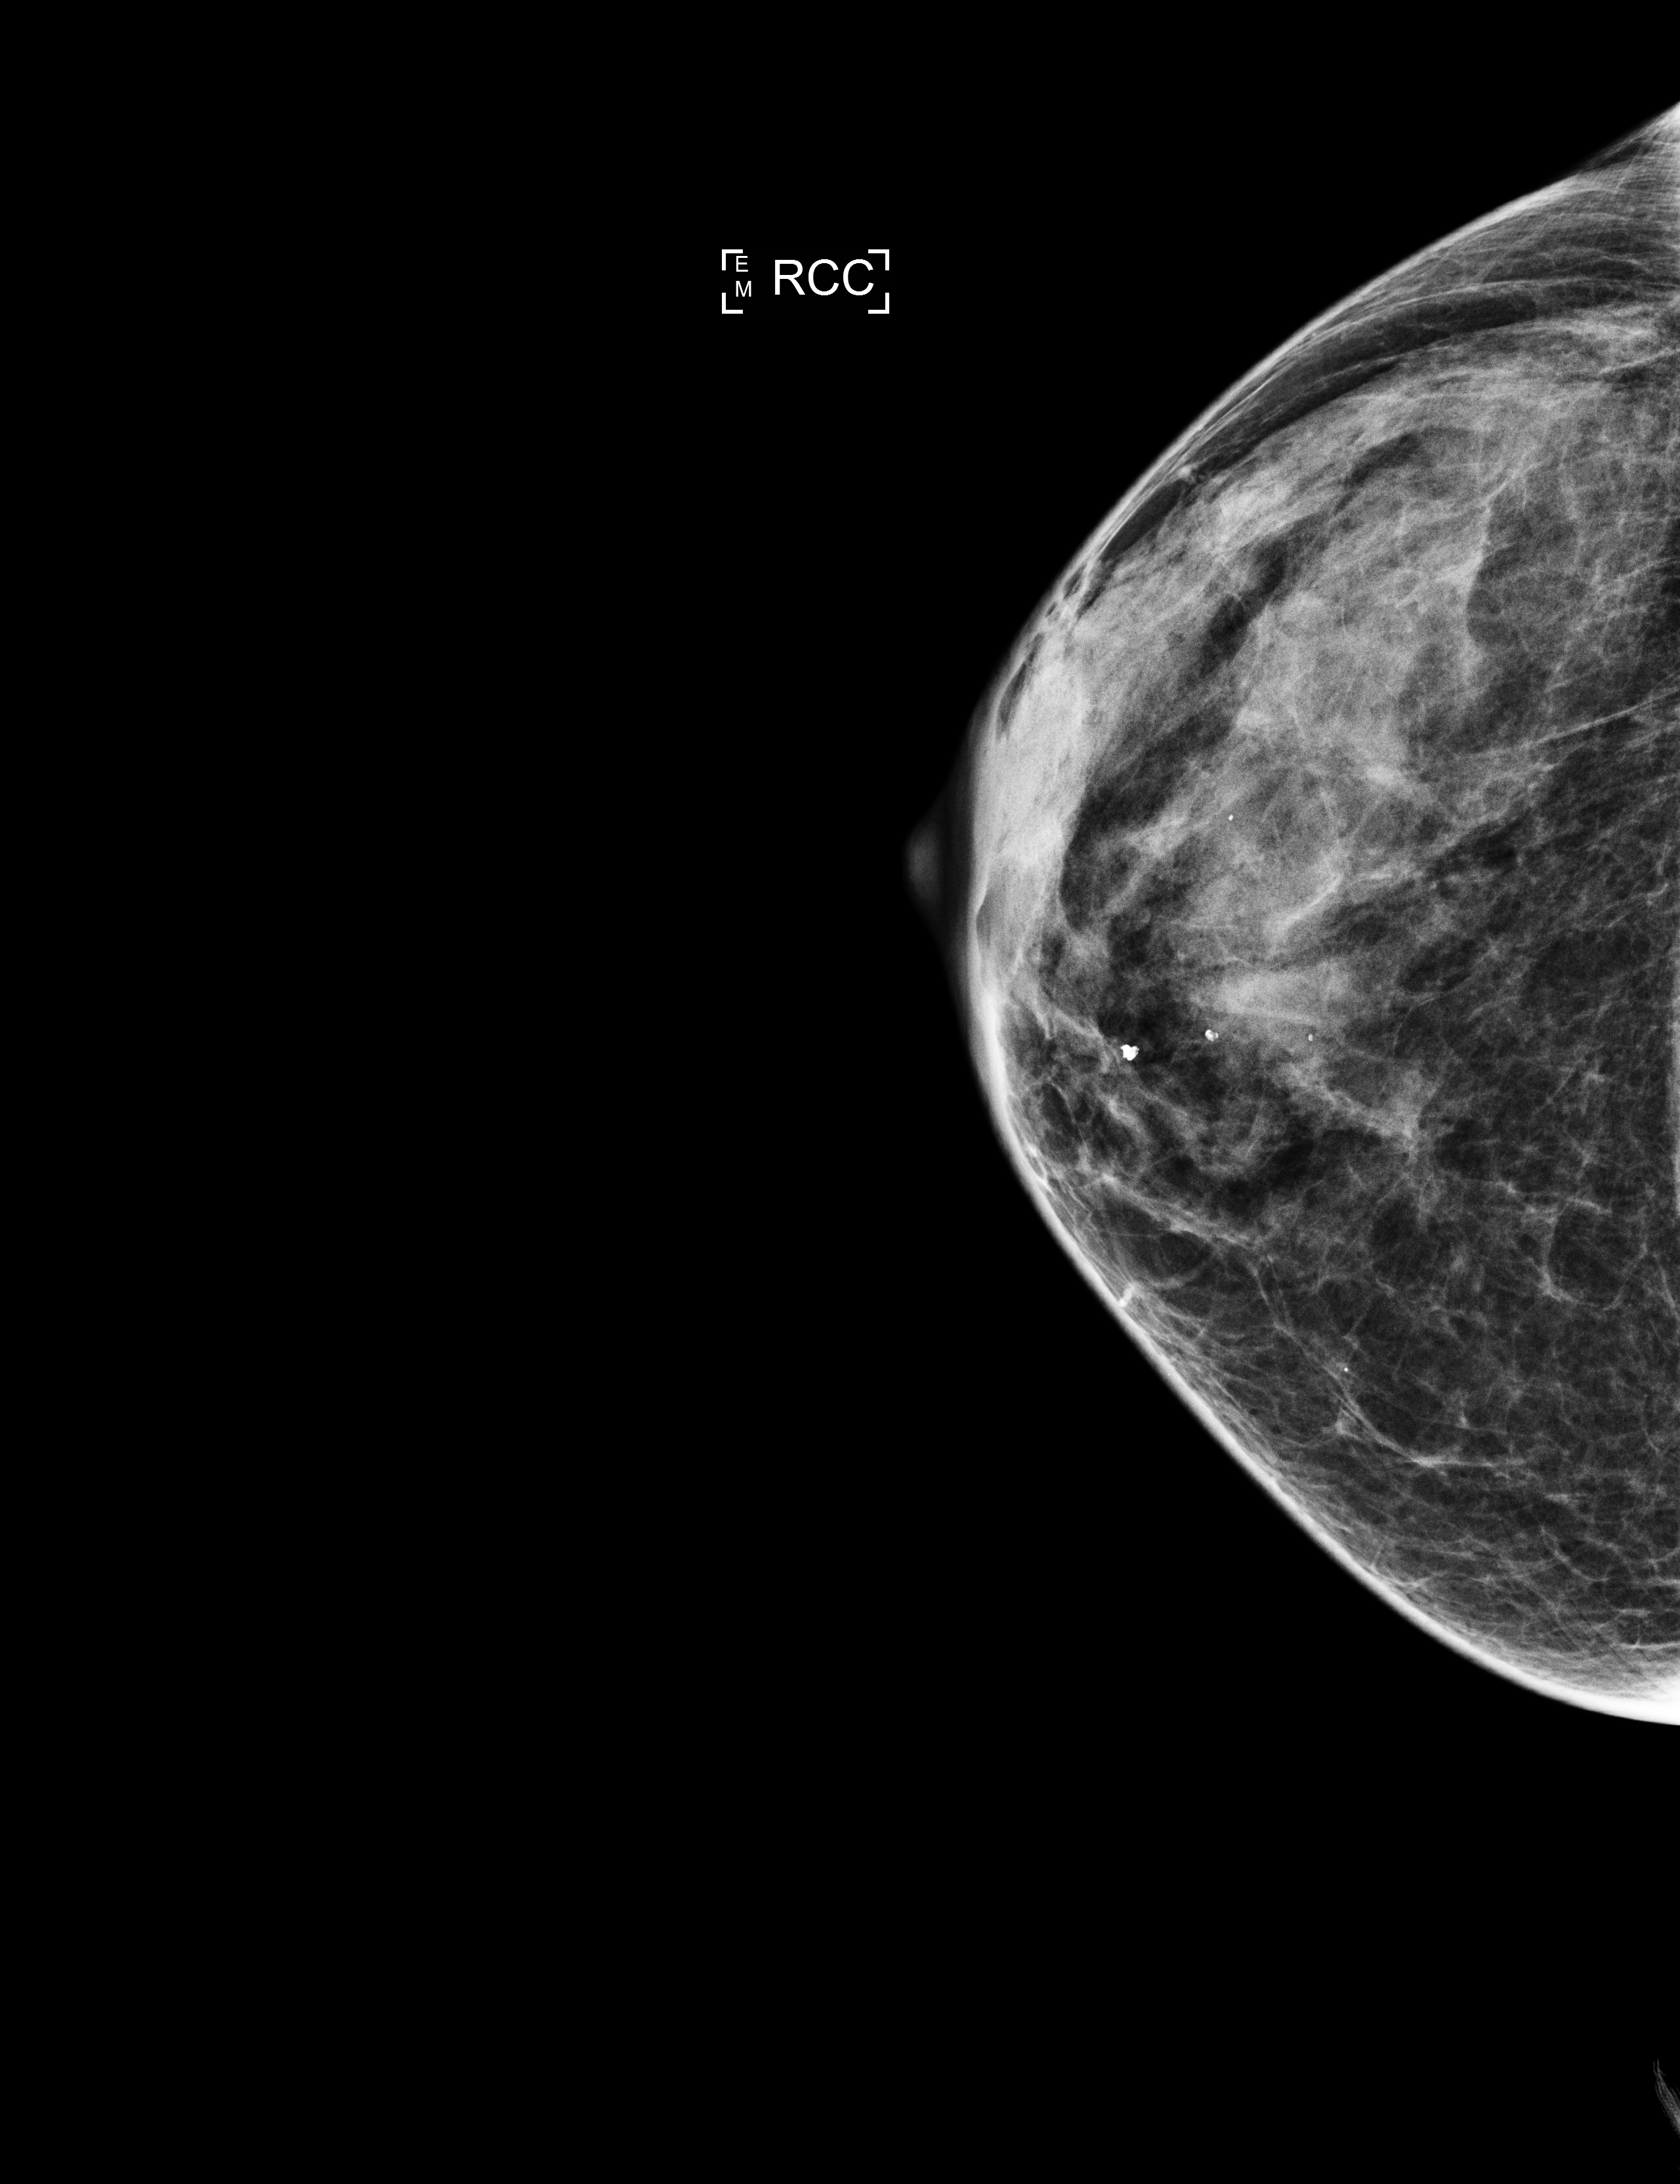
Screening examination; system: Selenia Dimensions. Female patient, age 66 years.
Image type: full-field digital mammogram. Breast: right. Projection: CC view.